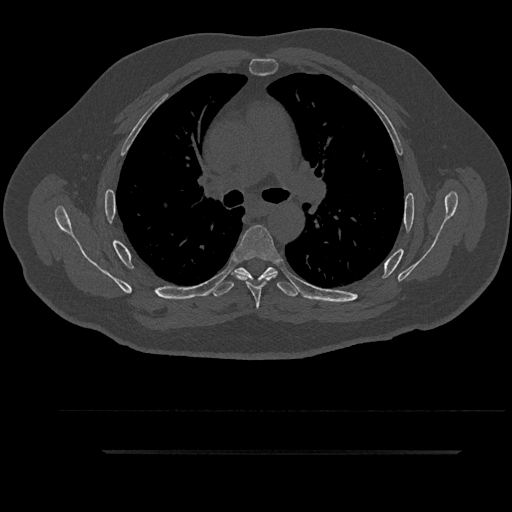
CT including the spine, one axial slice; slice 610 of 797 in the series (ordered by position); 120 kVp; bone window (W 1800 / L 400 HU); 0.5 mm slice thickness; 512 × 512 image matrix. Male patient, age 63 years. From the clinical record (not read from this slice): primary cancer: renal.
Outlined on this slice (semi-automatic segmentation, software-assisted and operator-edited):
- T5 vertebra: bounding box [x1, y1, x2, y2] px = [232, 225, 281, 309]
- T6 vertebra: [212, 267, 300, 297]